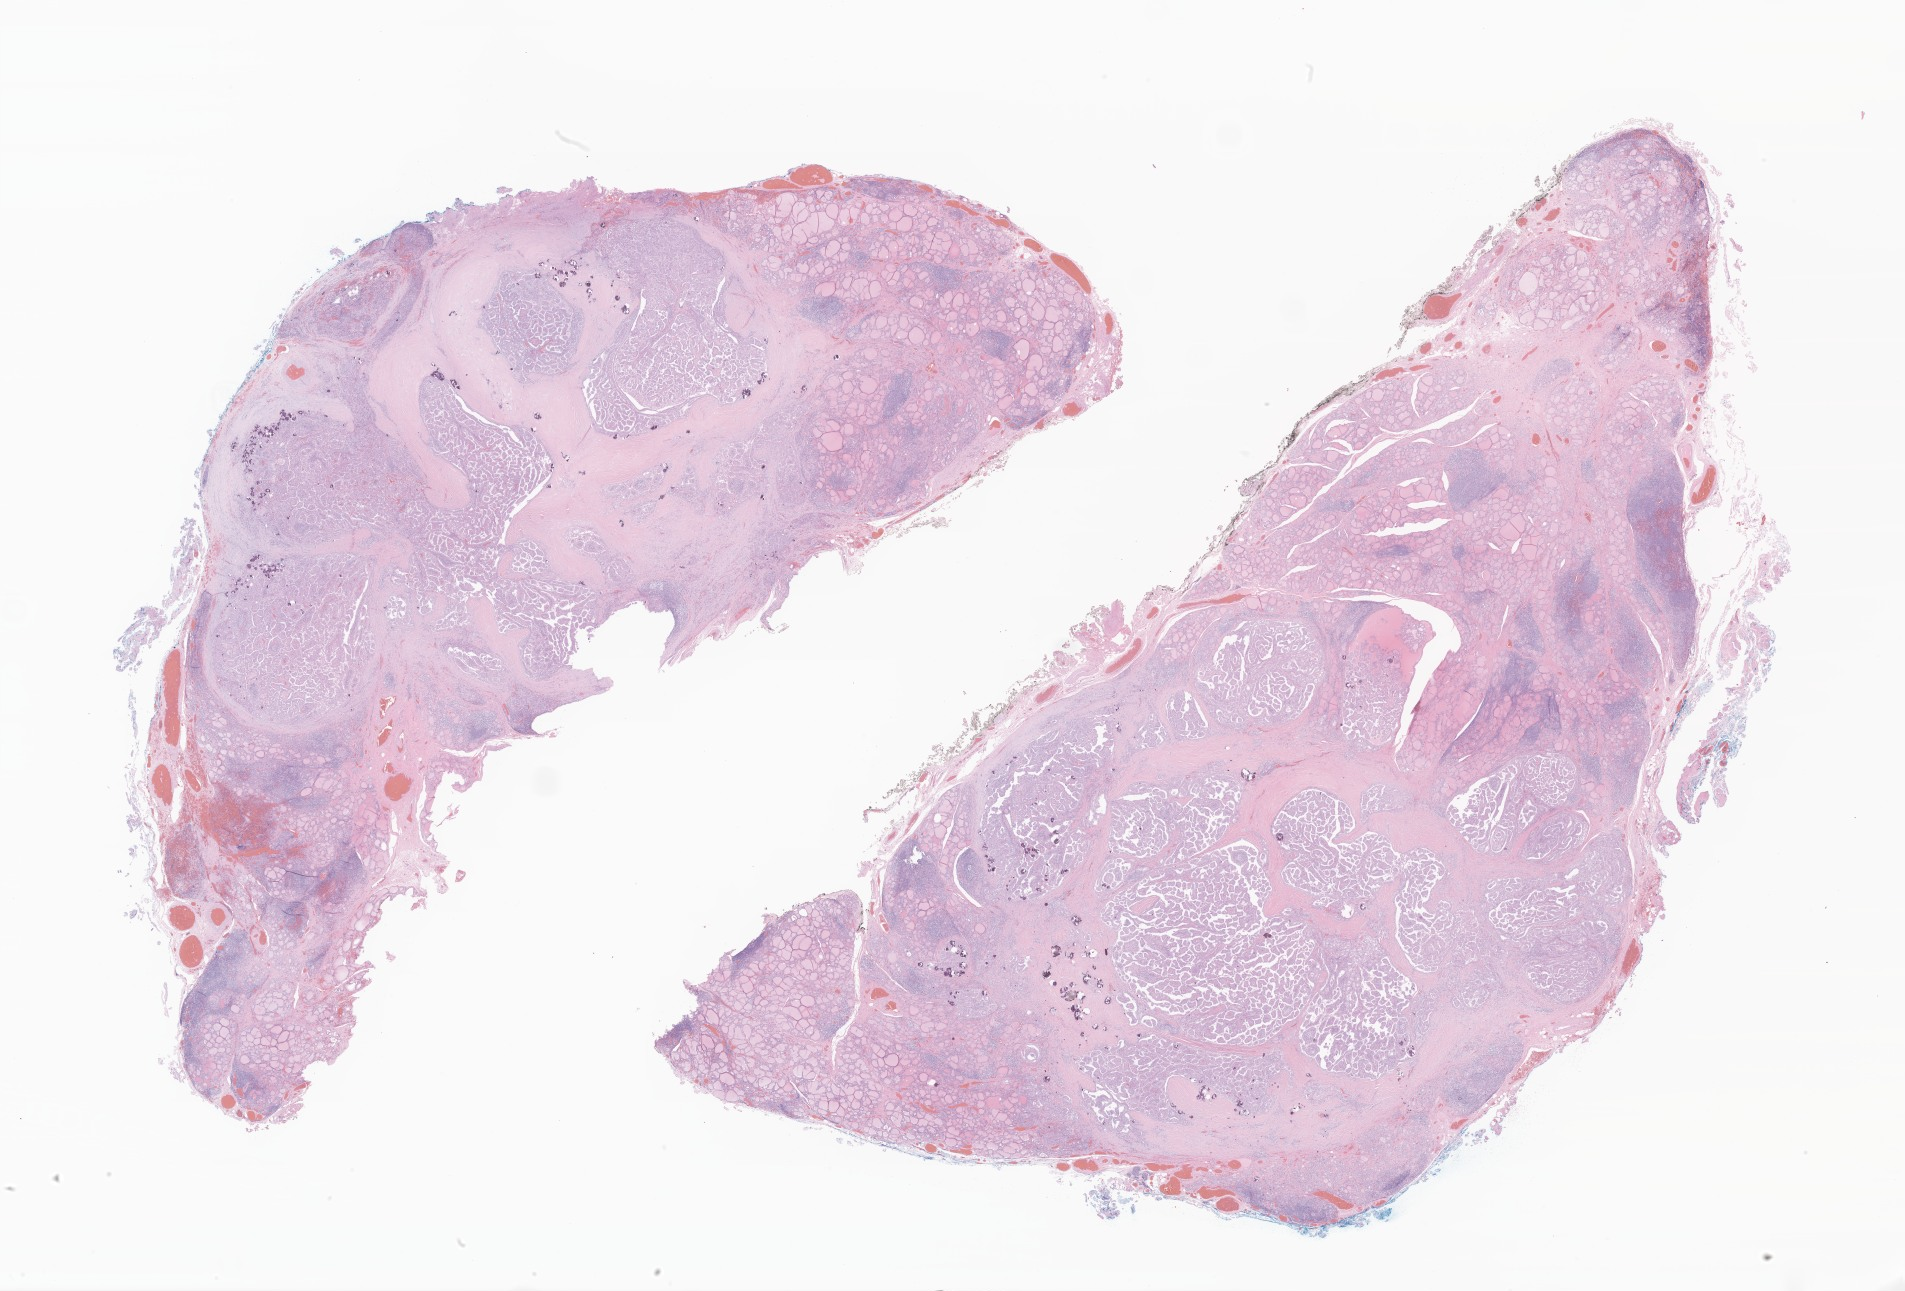
Whole-slide image, hematoxylin and eosin (H&E) stain of tumor tissue from the thyroid — a low-resolution overview of the entire scanned area, about 32.1 x 21.8 mm, formalin-fixed paraffin-embedded section. Patient: male, age 250 months (20 years 10 months).
Recorded diagnosis: Papillary carcinoma, NOS.